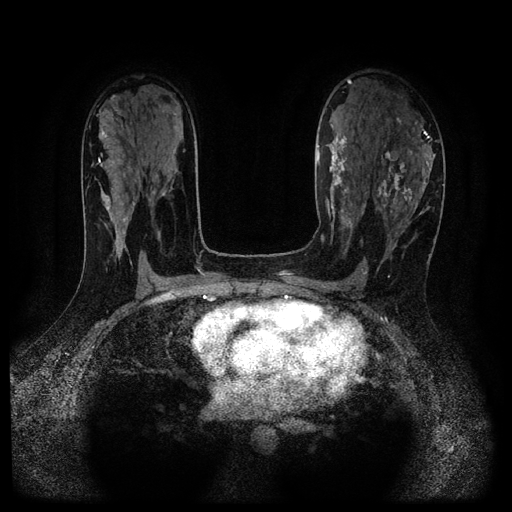
Breast MRI (dynamic contrast-enhanced, multi-phase), one axial slice; position 63 of 116 along the scan axis; dynamic contrast-enhanced series, time point 2 of 5 at this slice position (early post-contrast); 1.5 T; TE 2.7 ms, TR 5.4 ms; 512 × 512 image matrix, field of view 330 × 330 mm. Patient: female, 43 years.
Outlined on this slice (semi-automatically segmented with operator editing):
- breast lesion (labelled 'tumour' in the annotation; benign lesions carry a separate 'benign' label): bounding box (x1, y1, x2, y2) in pixels: (374, 126, 437, 226)
- breast lesion (labelled benign in the annotation): (321, 123, 360, 254)